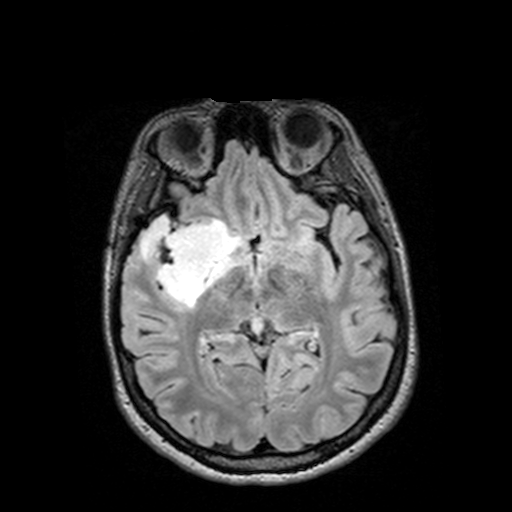
Brain MRI from a brain-tumour surgery series, one axial slice; position 77 of 144 along the scan axis; T2 FLAIR; 1 mm slice thickness; 512 × 512 image matrix, field of view 250 × 250 mm. From the clinical record (not read from this slice): histopathology: Astrocytoma; WHO grade: 3; IDH mutation: yes; tumour location: Right Insular Temporal.
Outlined on this slice (outlined manually by an expert reader):
- tumour: bounding box <126,218,232,305> (left, top, right, bottom; pixels)